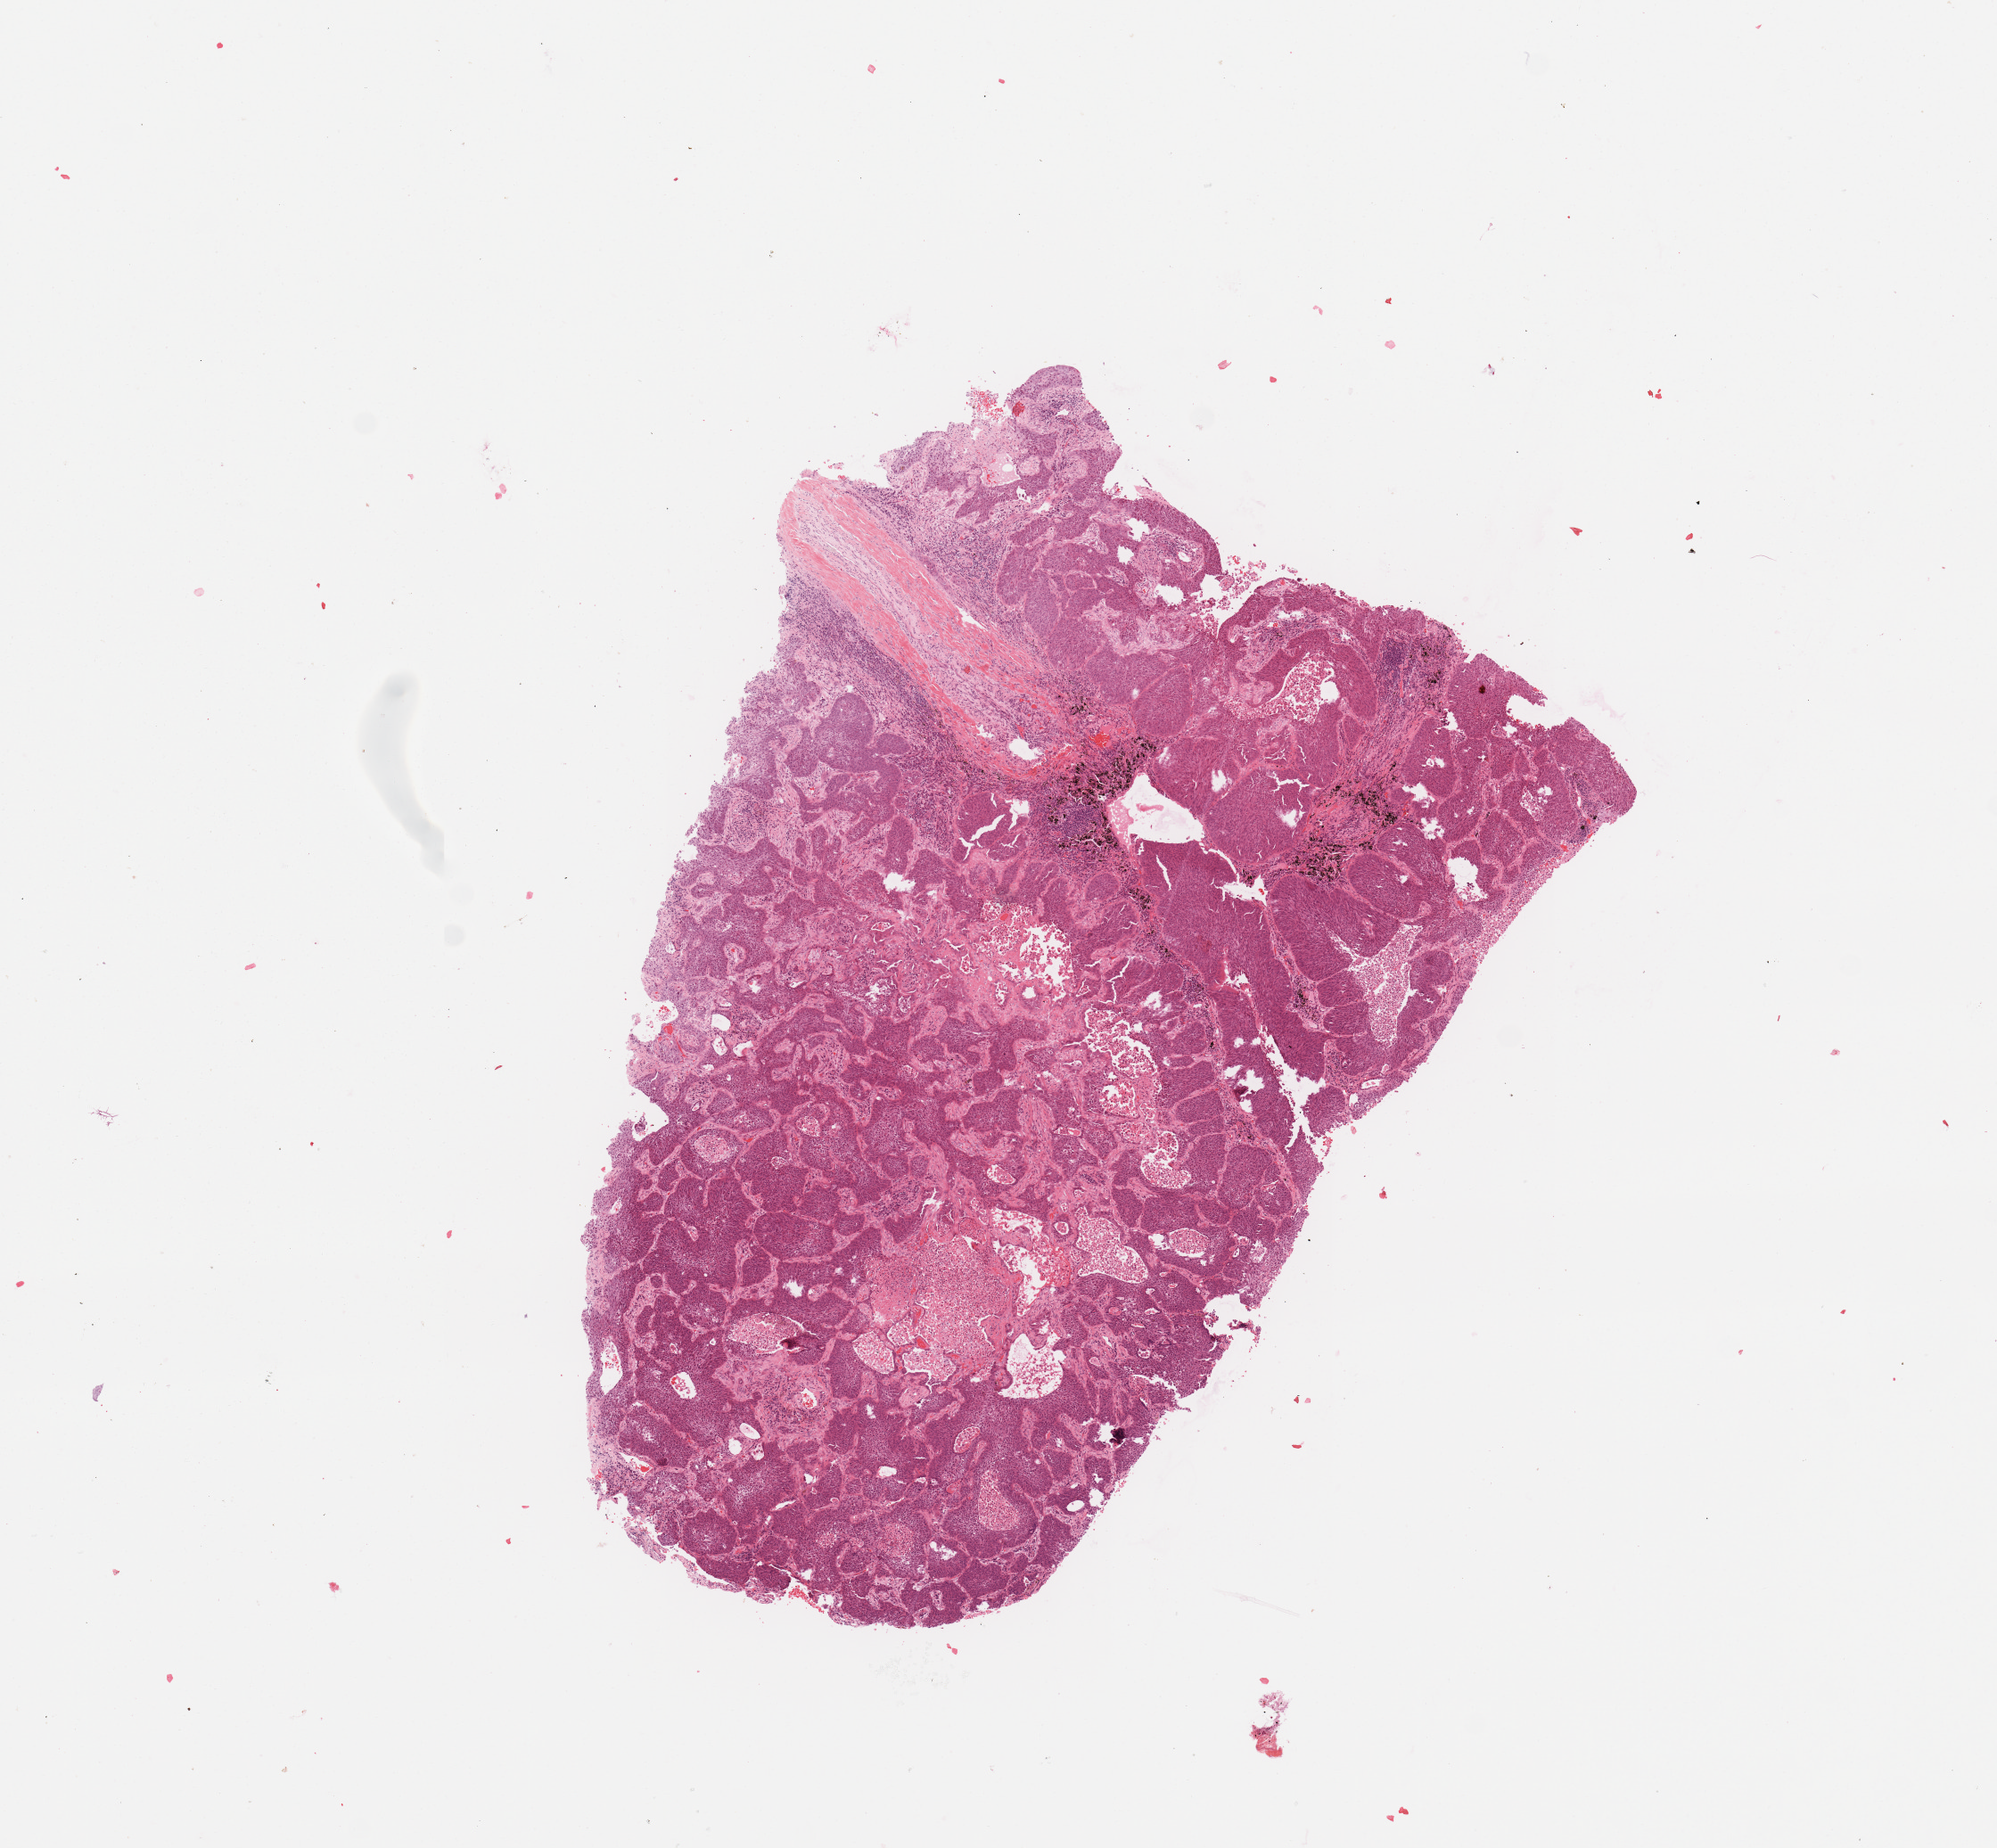
H&E-stained whole-slide image, whole scanned area (about 8.9 x 8.2 mm, acquisition: 20x scan) shown as a low-resolution overview, lung, tumour tissue. Patient: male, age 62 years. Histologic grade: G2 (moderately differentiated).
- diagnosis: Squamous cell carcinoma, NOS
- AJCC pathologic stage: IA3
- primary tumour site (as recorded): right upper lobe